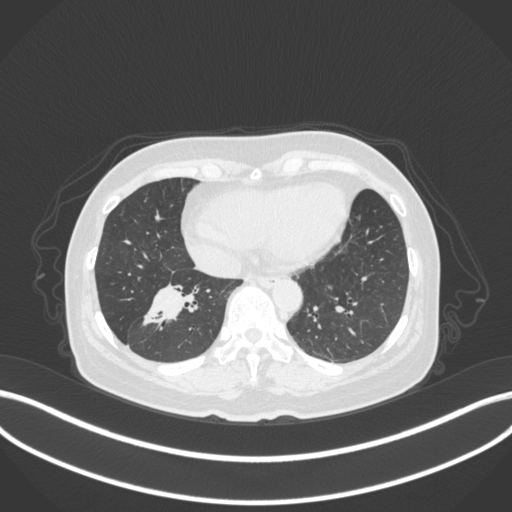
Chest CT, one axial slice; position 126 of 429 along the scan axis; reconstruction kernel B31f; 120 kVp; lung window (W 1500 / L -600 HU); 512 × 512 image matrix. Patient: female, 67 years. From the clinical record (not read from this slice): clinical TNM (as recorded): T1c N1 M0; histopathological grade: G2-3.
Annotated regions visible in this slice (rectangle marked by the reading radiologist):
- lung tumour (recorded histology: adenocarcinoma): bounding box (x1, y1, x2, y2) in pixels: (142, 278, 205, 328)